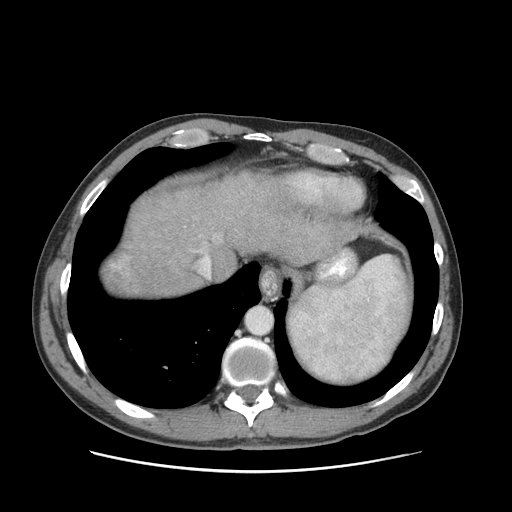
Contrast-enhanced abdominal CT (liver protocol), one axial slice; position 82 of 93 along the scan axis; soft-tissue window (W 400 / L 40 HU); 2.5 mm slice thickness; 512 × 512 image matrix, field of view 380 × 380 mm. From the clinical record (not read from this slice): diagnosis: hepatocellular carcinoma (patient treated with transarterial chemoembolisation; whether this scan precedes or follows treatment is not stated here); TNM stage (as recorded): Stage-II; Child-Pugh class: A; tumour differentiation: moderately differentiated; tumour size: 1 cm.
Outlined on this slice (semi-automatic segmentation, software-assisted and operator-edited):
- abdominal aorta: bounding box [x1, y1, x2, y2] px = [245, 307, 272, 335]
- liver parenchyma outside the tumour (the mass and vessels are separate outlines, so this box may not span the whole liver): [108, 172, 348, 296]
- mass: [110, 265, 132, 287]
- liver vessels: [201, 256, 210, 265]